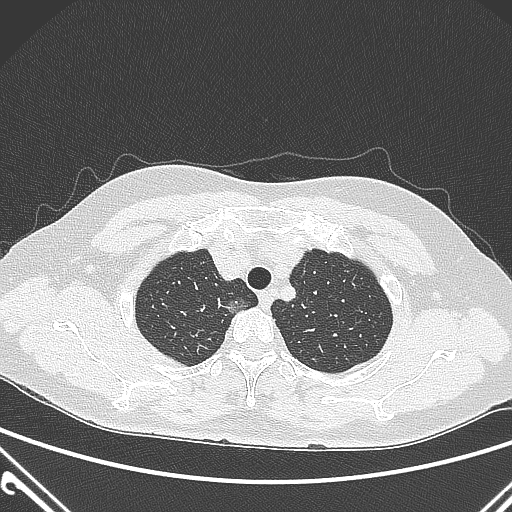
Chest CT, one axial slice; slice 241 of 300 in the series (ordered by position); lung window (W 1500 / L -600 HU); 1 mm slice thickness; 512 × 512 image matrix. Patient: female, 54 years. From the clinical record (not read from this slice): clinical TNM (as recorded): T1a N0 M0; histopathological grade: G1.
Outlined on this slice (bounding box drawn by a radiologist):
- lung tumour (recorded histology: adenocarcinoma): bounding box <217,292,259,322> (left, top, right, bottom; pixels)